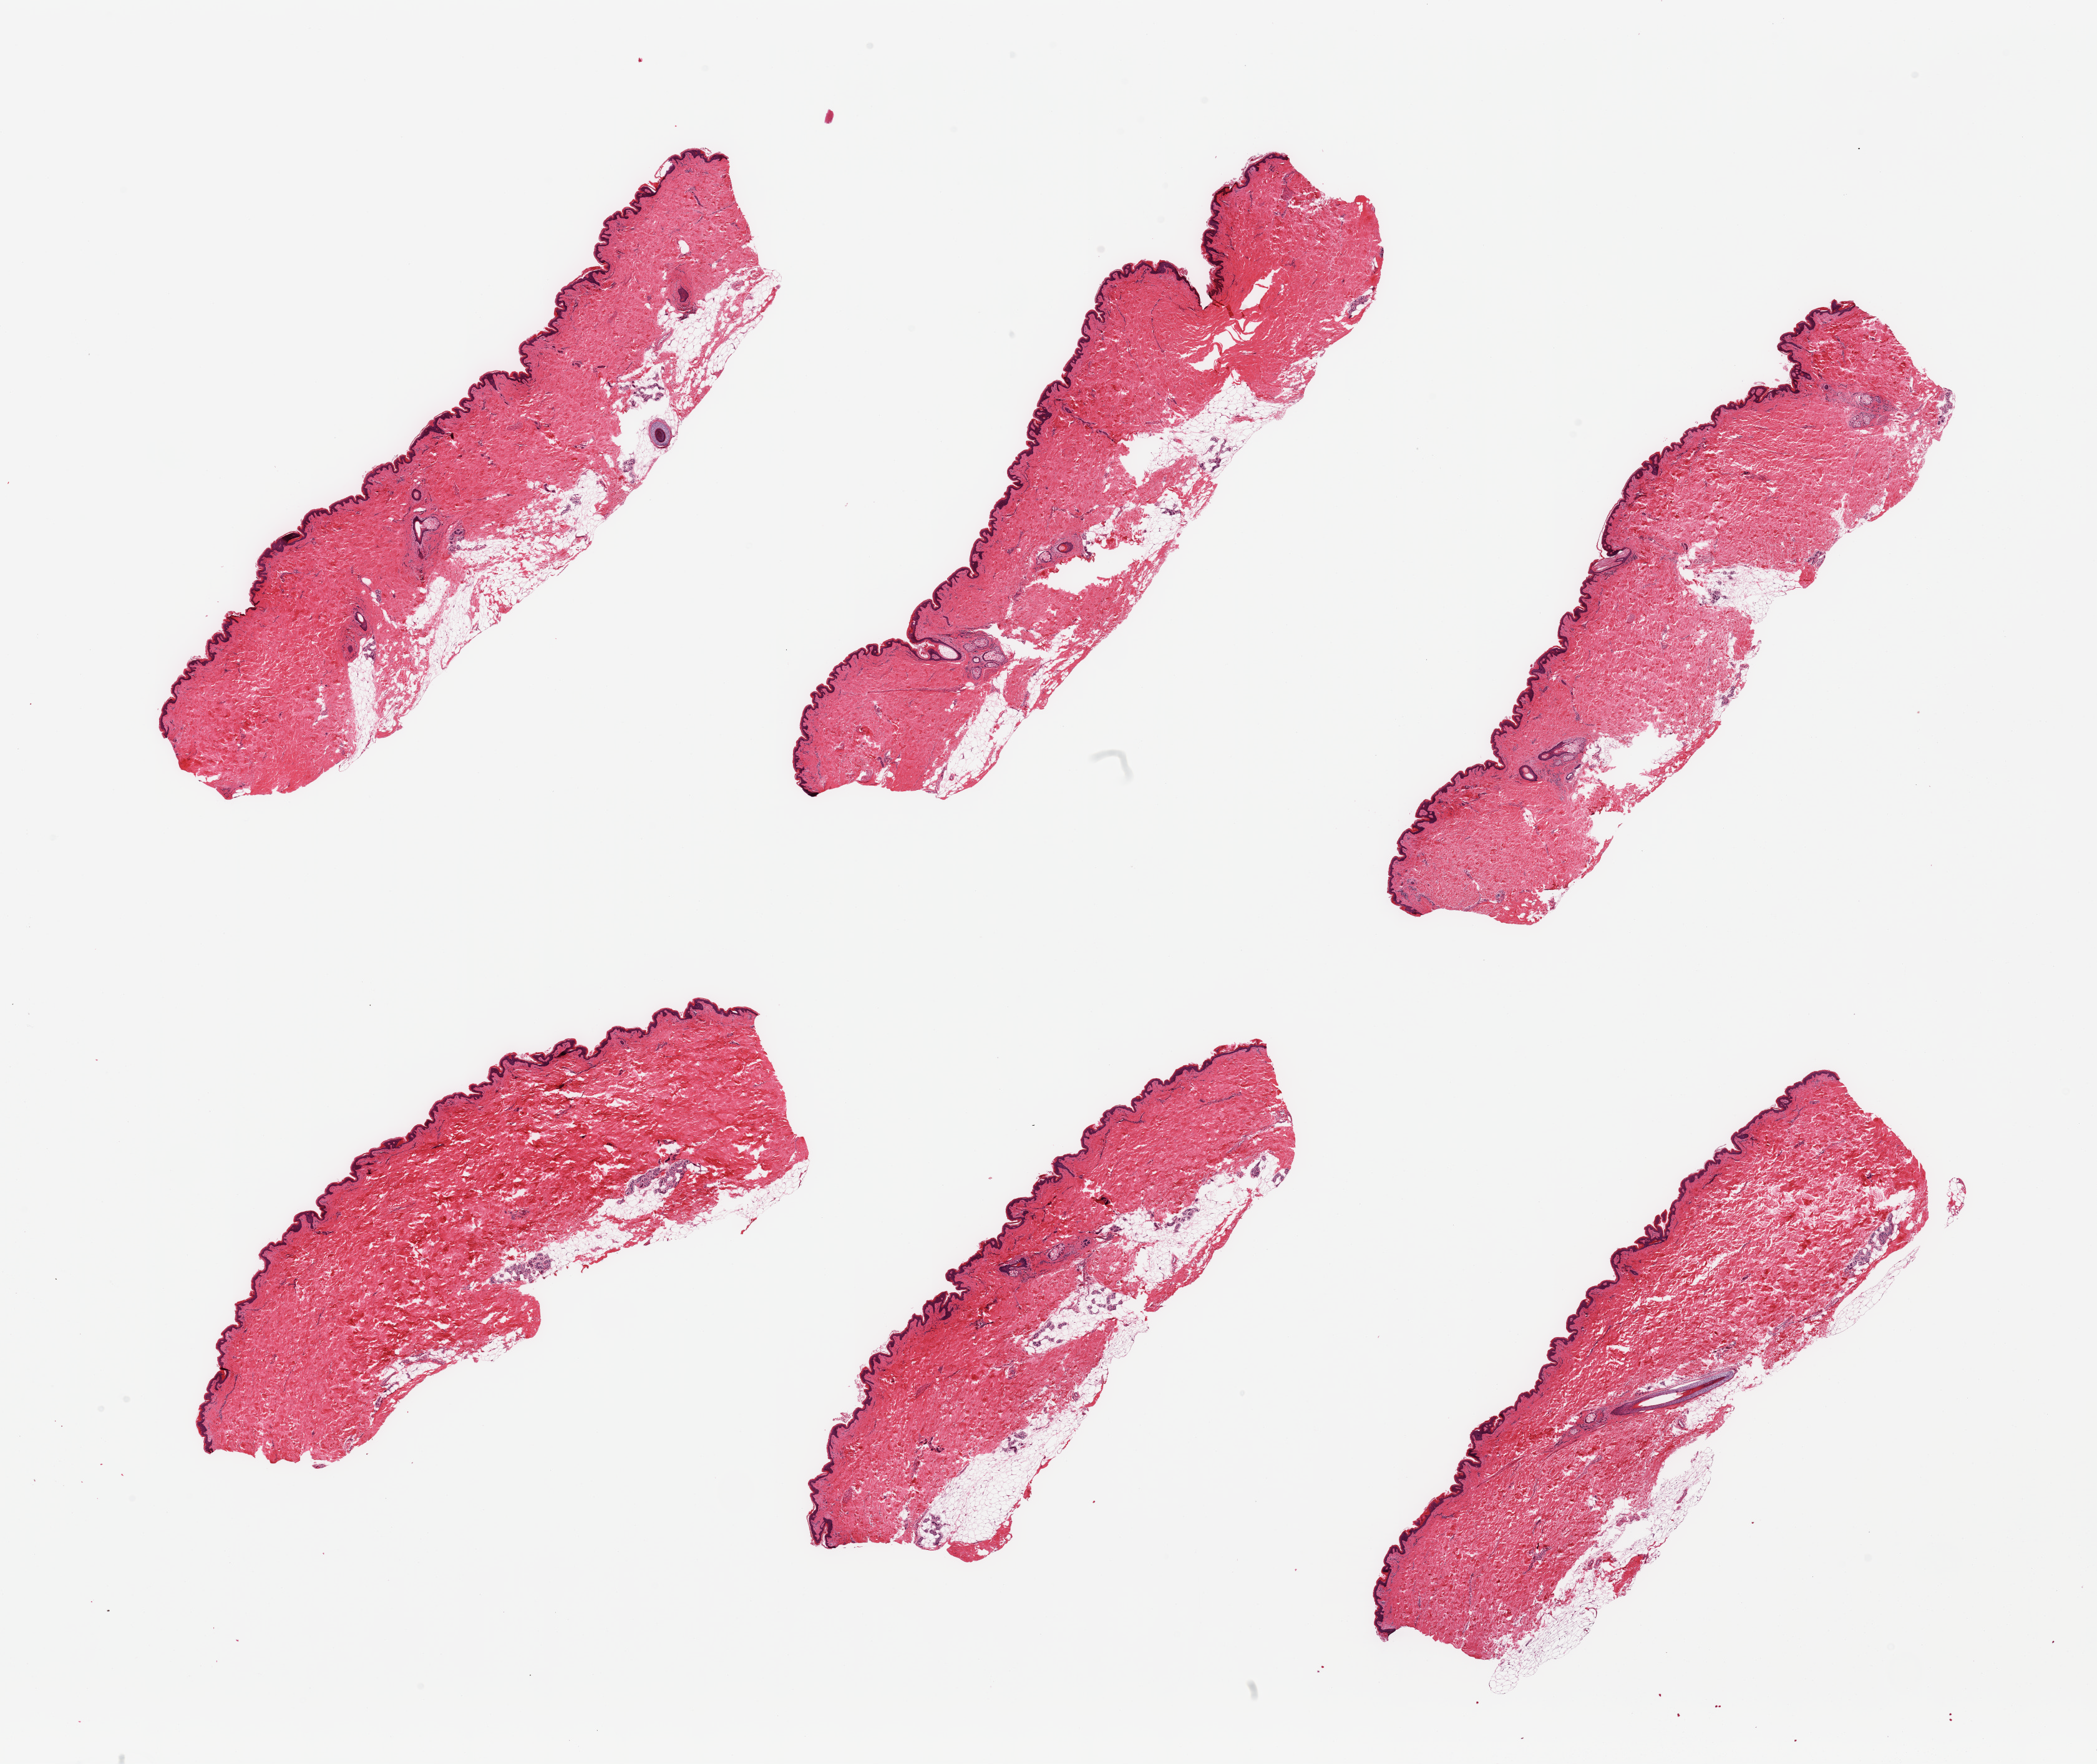
Haematoxylin and eosin whole-slide image — whole scanned area (about 26.6 x 22.4 mm, slide scanned at 20x) shown as a low-resolution overview. PAXgene-fixed, paraffin-embedded tissue. Section of skin of suprapubic region (target tissue). Donor tissue sample. Donor sex: male.
* reviewer comment on this tissue sample: 6 pieces; 10 to 20% dermal fat